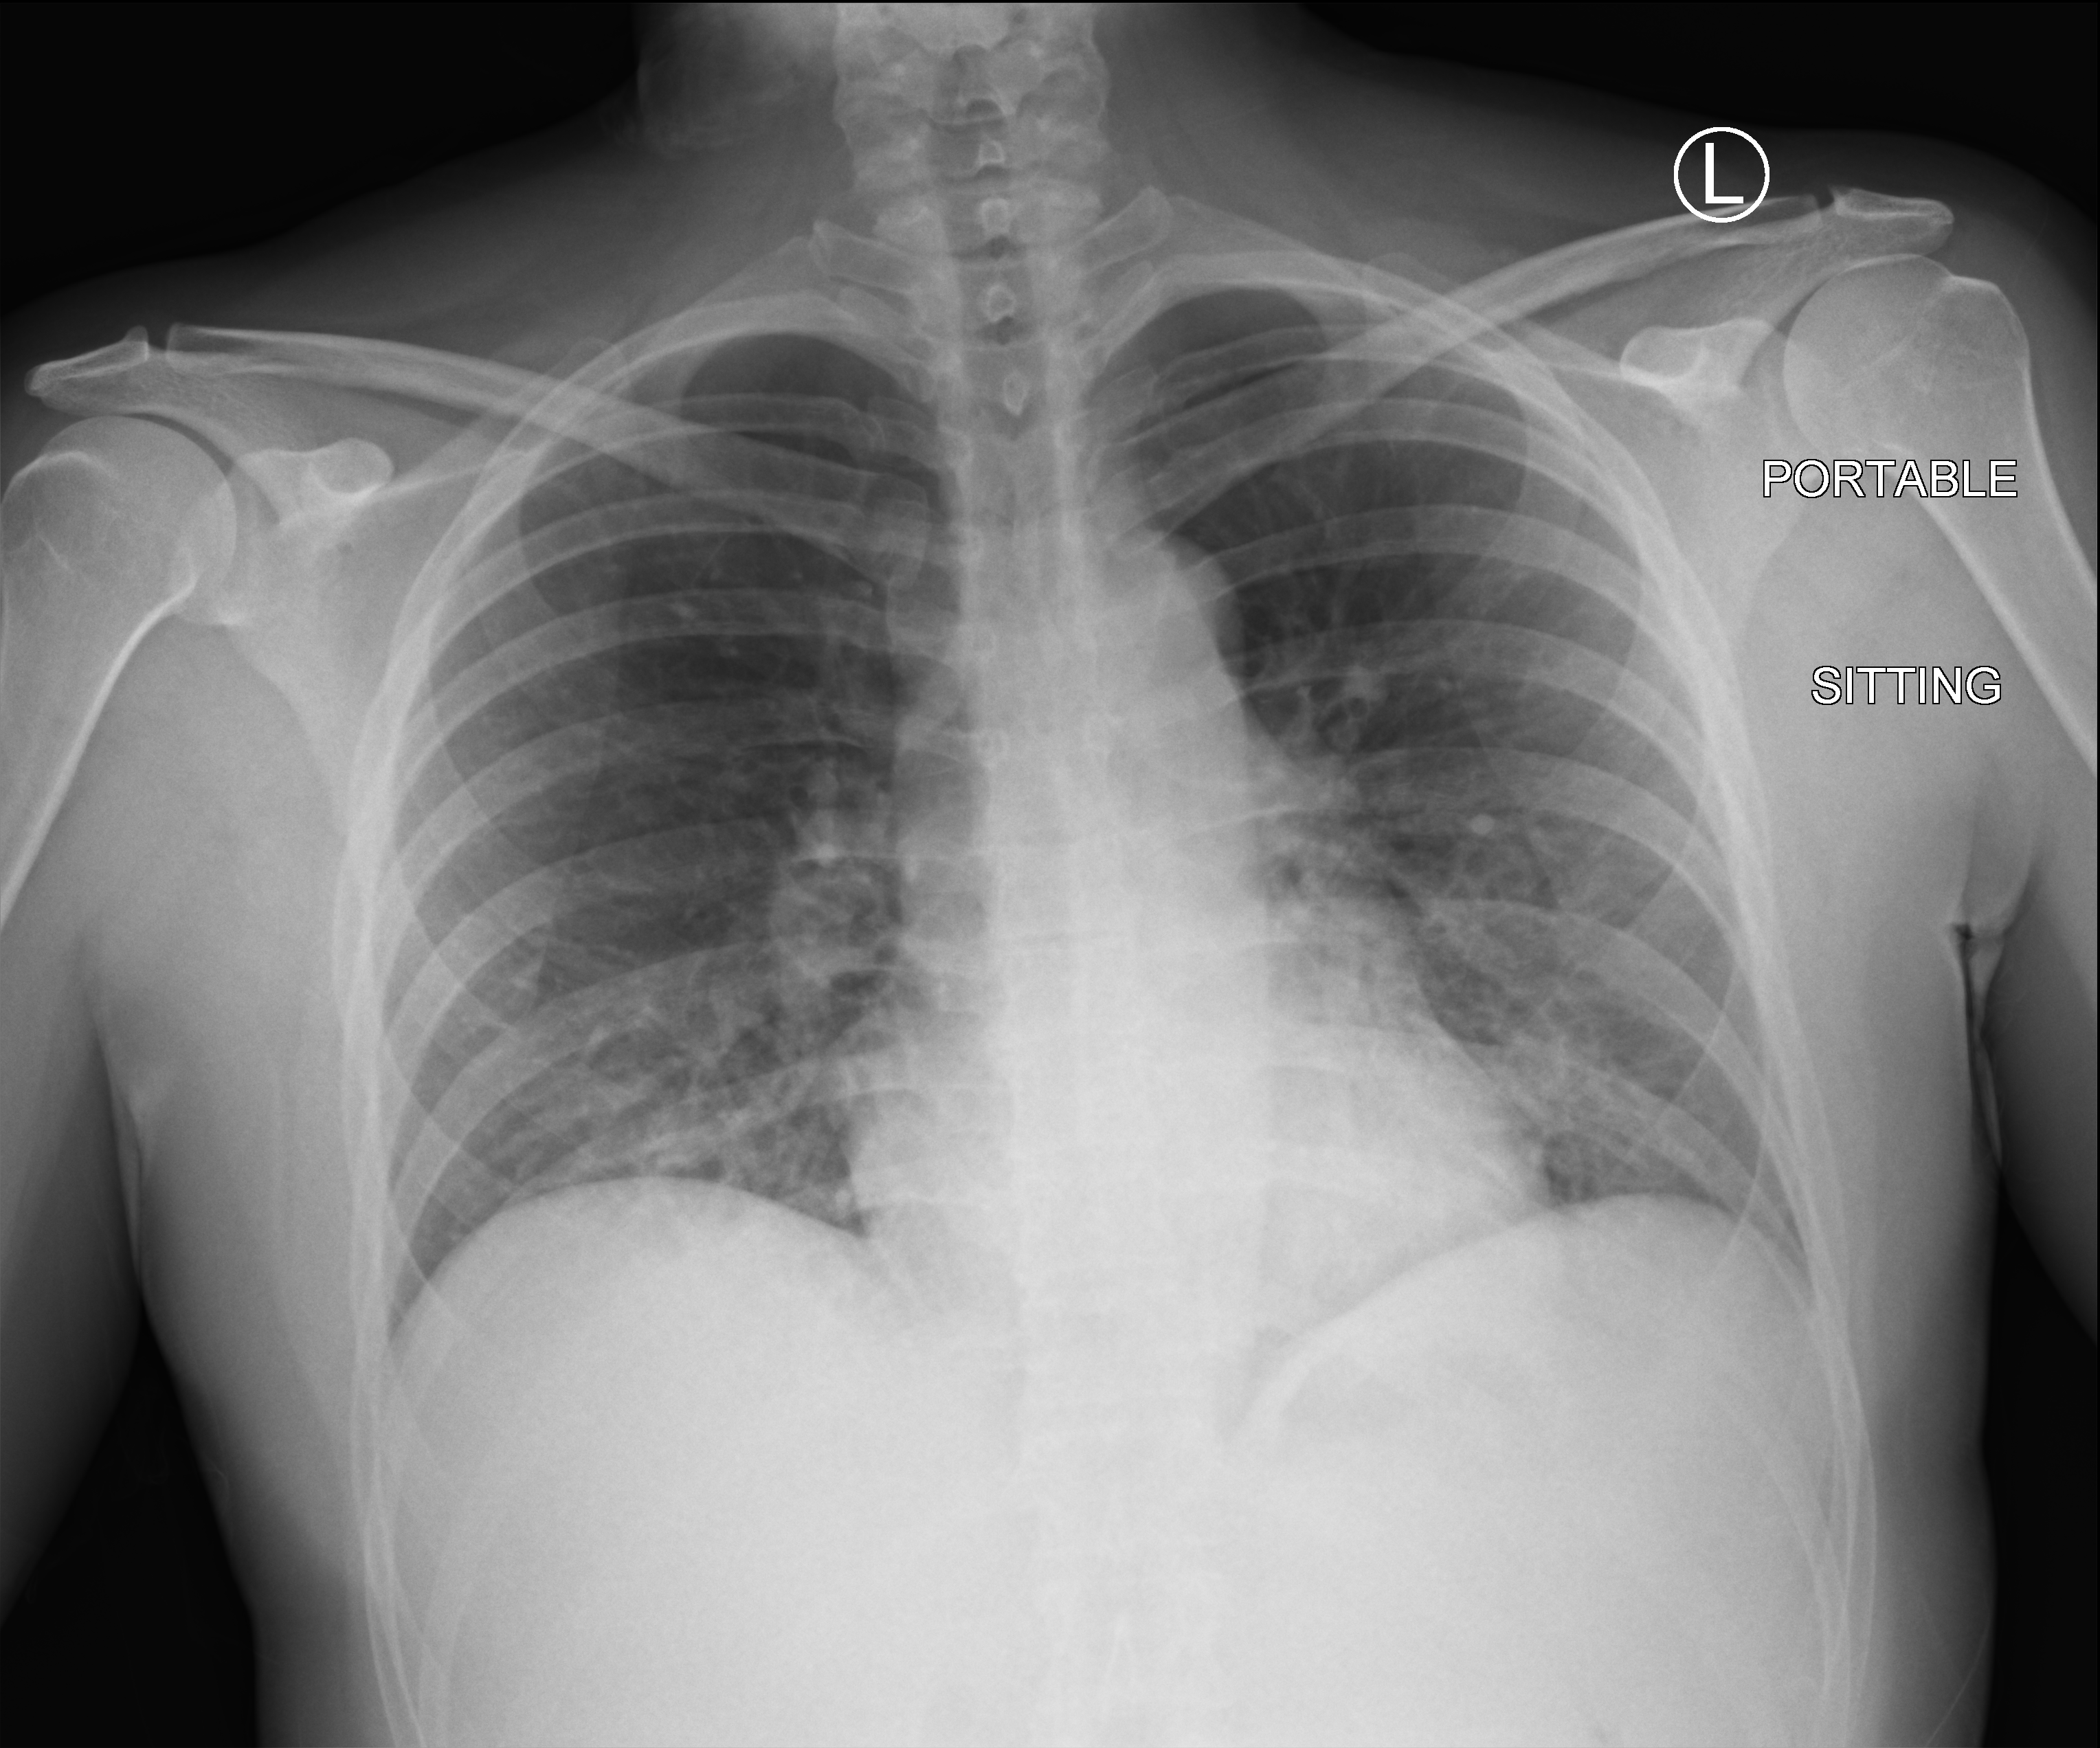
Chest X-ray (portable), anteroposterior (AP) projection. Patient hospitalised with COVID-19; female, aged 18–59 years.
Hospital-stay facts (about this admission, not read from this image; timing relative to this image not recorded):
- admitted to intensive care during this hospital stay: no
- mechanically ventilated during this hospital stay: no
- length of hospital stay: 1 day